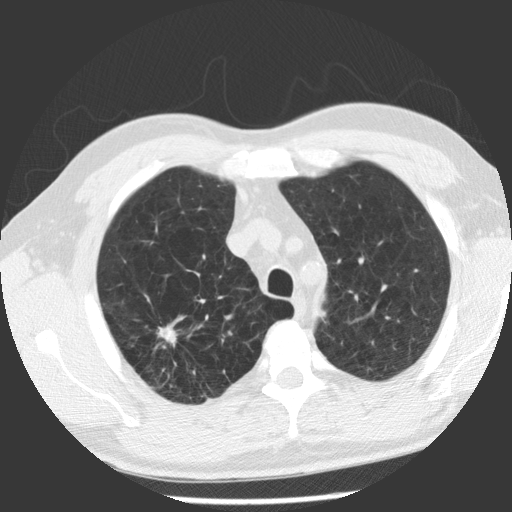
Low-dose screening chest CT, one axial slice. Slice 89 of 112 in the series (ordered by position). Reconstruction kernel STANDARD. Lung window (W 1500 / L -600 HU). 2.5 mm slice thickness. 512 × 512 image matrix, field of view 344 × 344 mm.
Structures marked on this image (outlined manually by an expert reader):
- lesion 1 (tumor, upper lobe of right lung): bounding box (x1, y1, x2, y2) in pixels: (157, 325, 177, 345)